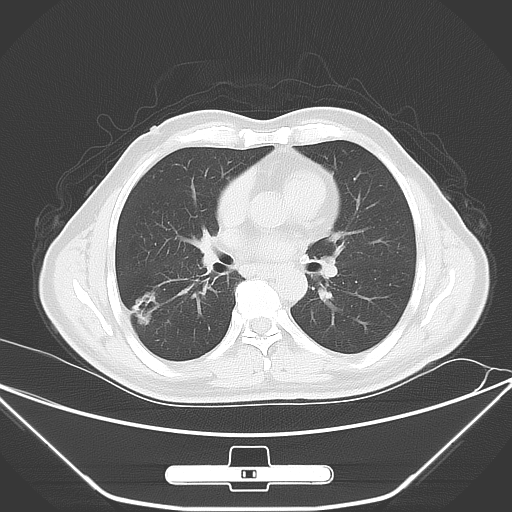
Chest CT, one axial slice. Position 30 of 62 along the scan axis. 120 kVp. Lung window (W 1500 / L -600 HU). 5 mm slice thickness. 512 × 512 image matrix, field of view 398 × 398 mm. Male patient, age 71 years. From the clinical record (not read from this slice): clinical TNM (as recorded): T1c N0 M0; histopathological grade: G2.
Structures marked on this image (bounding box drawn by a radiologist):
- lung tumour (recorded histology: adenocarcinoma): bounding box [x1, y1, x2, y2] px = [131, 286, 161, 335]